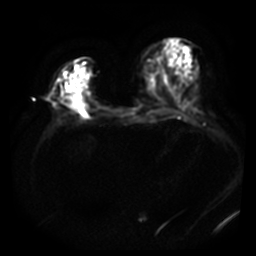
Breast MRI, one axial slice. Diffusion-weighted series; image 2 of 4 stored at this slice position (different b-values; order by instance number). 3 T. 5 mm slice thickness. 256 × 256 image matrix, field of view 380 × 380 mm. Female patient.
Structures marked on this image (manually delineated by an expert):
- tumour on diffusion-weighted imaging: bounding box (x1, y1, x2, y2) in pixels: (65, 95, 73, 104)